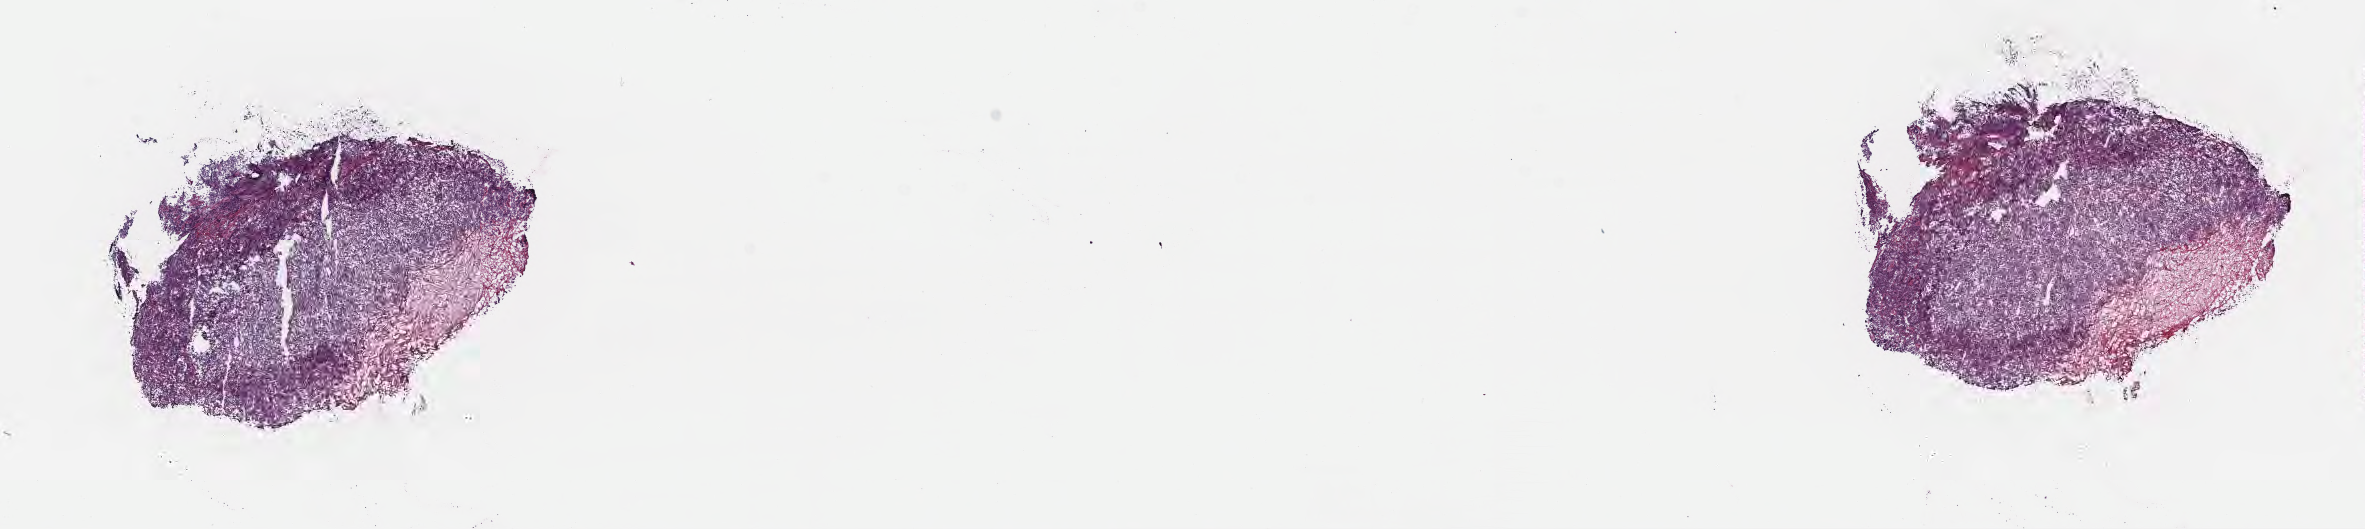
Digitized haematoxylin and eosin-stained section — a low-resolution overview of the entire scanned area, about 19.1 x 4.3 mm; frozen section; primary tumor; site: cranium. Female patient; age at initial diagnosis 3 years.
Histologic diagnosis: Burkitt lymphoma, NOS.